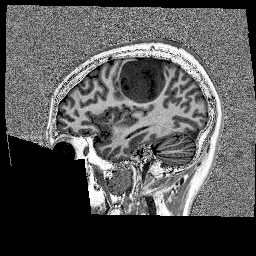
Brain MRI from a brain-tumour surgery series, one sagittal slice; slice 52 of 176 in the series (ordered by position); 256 × 256 image matrix. Case-level facts recorded for this patient, not image findings: histopathology: Glioblastoma; WHO grade: 4; IDH mutation: no; tumour location: Left Frontal.
Structures marked on this image (outlined manually by an expert reader):
- tumour: bounding box [x1, y1, x2, y2] px = [123, 58, 169, 105]